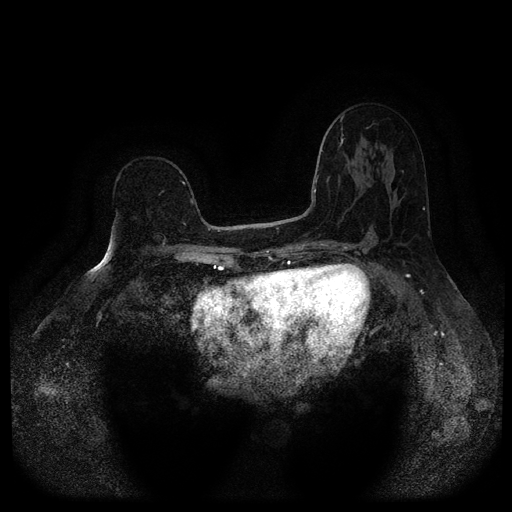
Breast MRI (dynamic contrast-enhanced, multi-phase), one axial slice; position 64 of 116 along the scan axis; dynamic contrast-enhanced series, time point 2 of 5 at this slice position (early post-contrast); 1.5 T; TE 2.6 ms, TR 5.4 ms; 2 mm slice thickness; 512 × 512 image matrix, field of view 340 × 340 mm. Female patient, age 64 years.
Annotated regions visible in this slice (semi-automatic segmentation, software-assisted and operator-edited):
- breast lesion (labelled benign in the annotation): bounding box (x1, y1, x2, y2) in pixels: (152, 229, 169, 247)